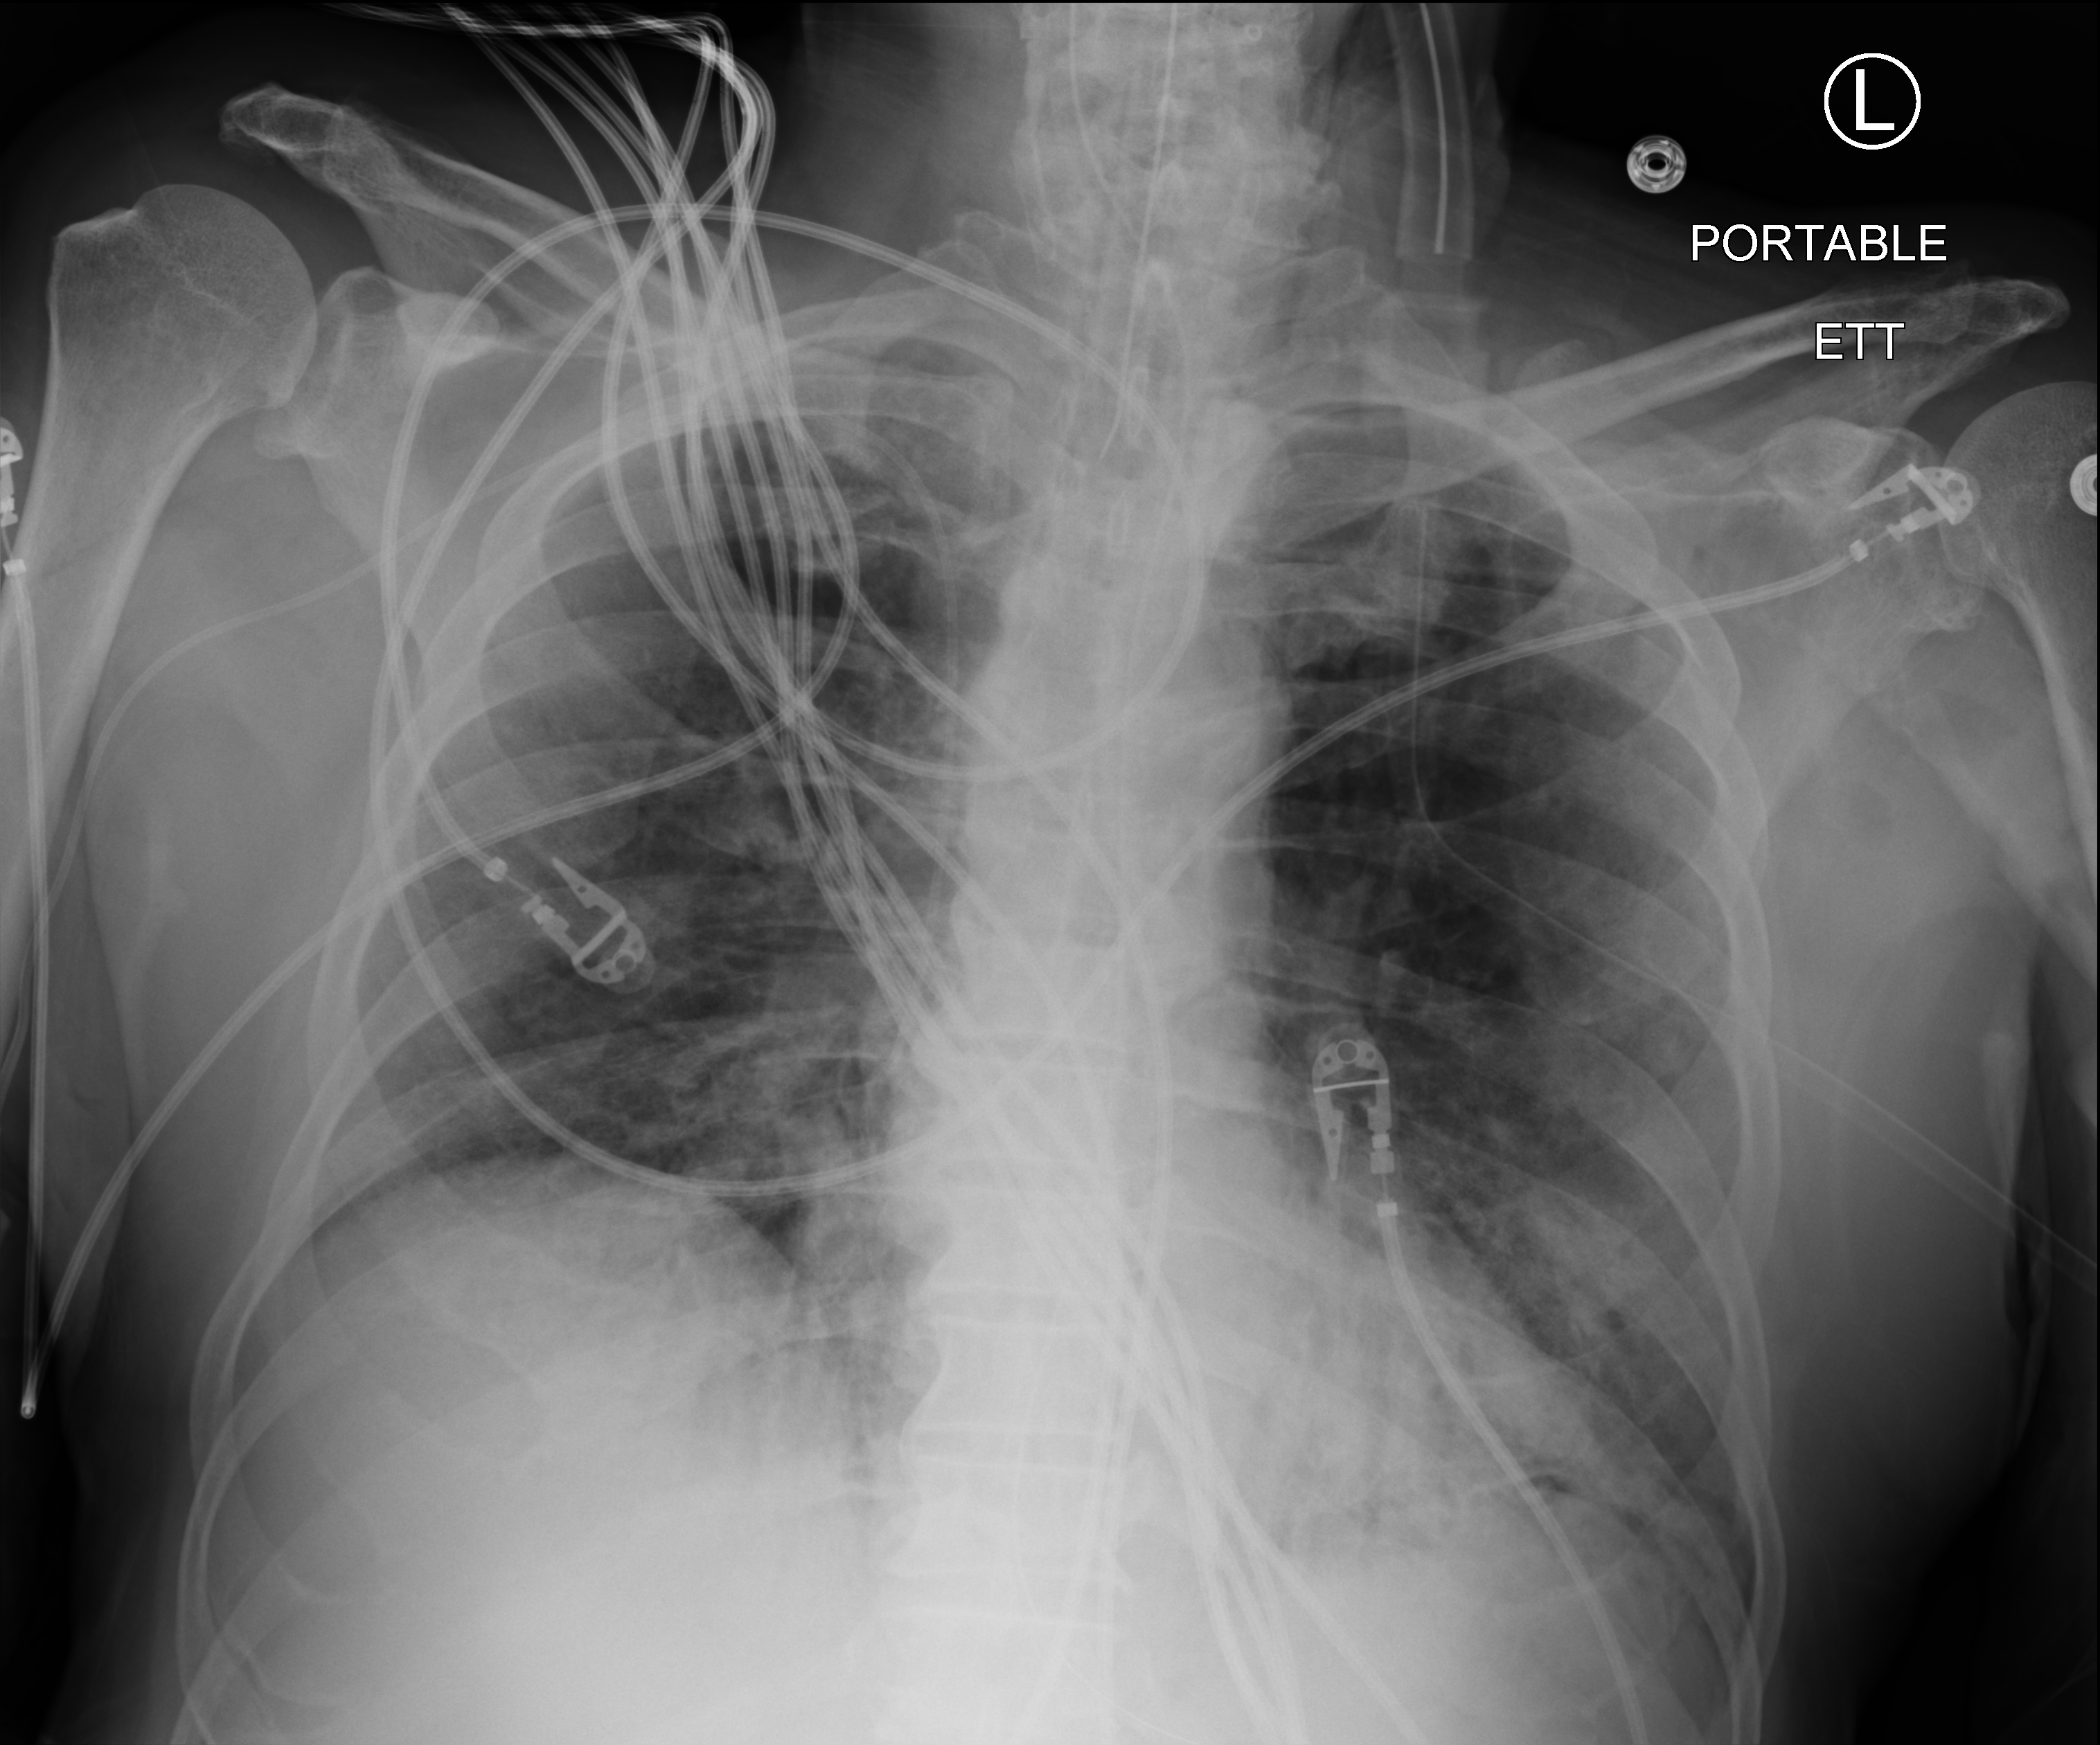
Portable chest radiograph, anteroposterior (AP) projection. Patient hospitalised with COVID-19; male, aged 75–90 years.
From the hospital-stay record, not from the radiograph (when in the stay this image was taken is not recorded):
- diabetes (admission record): no
- length of hospital stay: 33 days